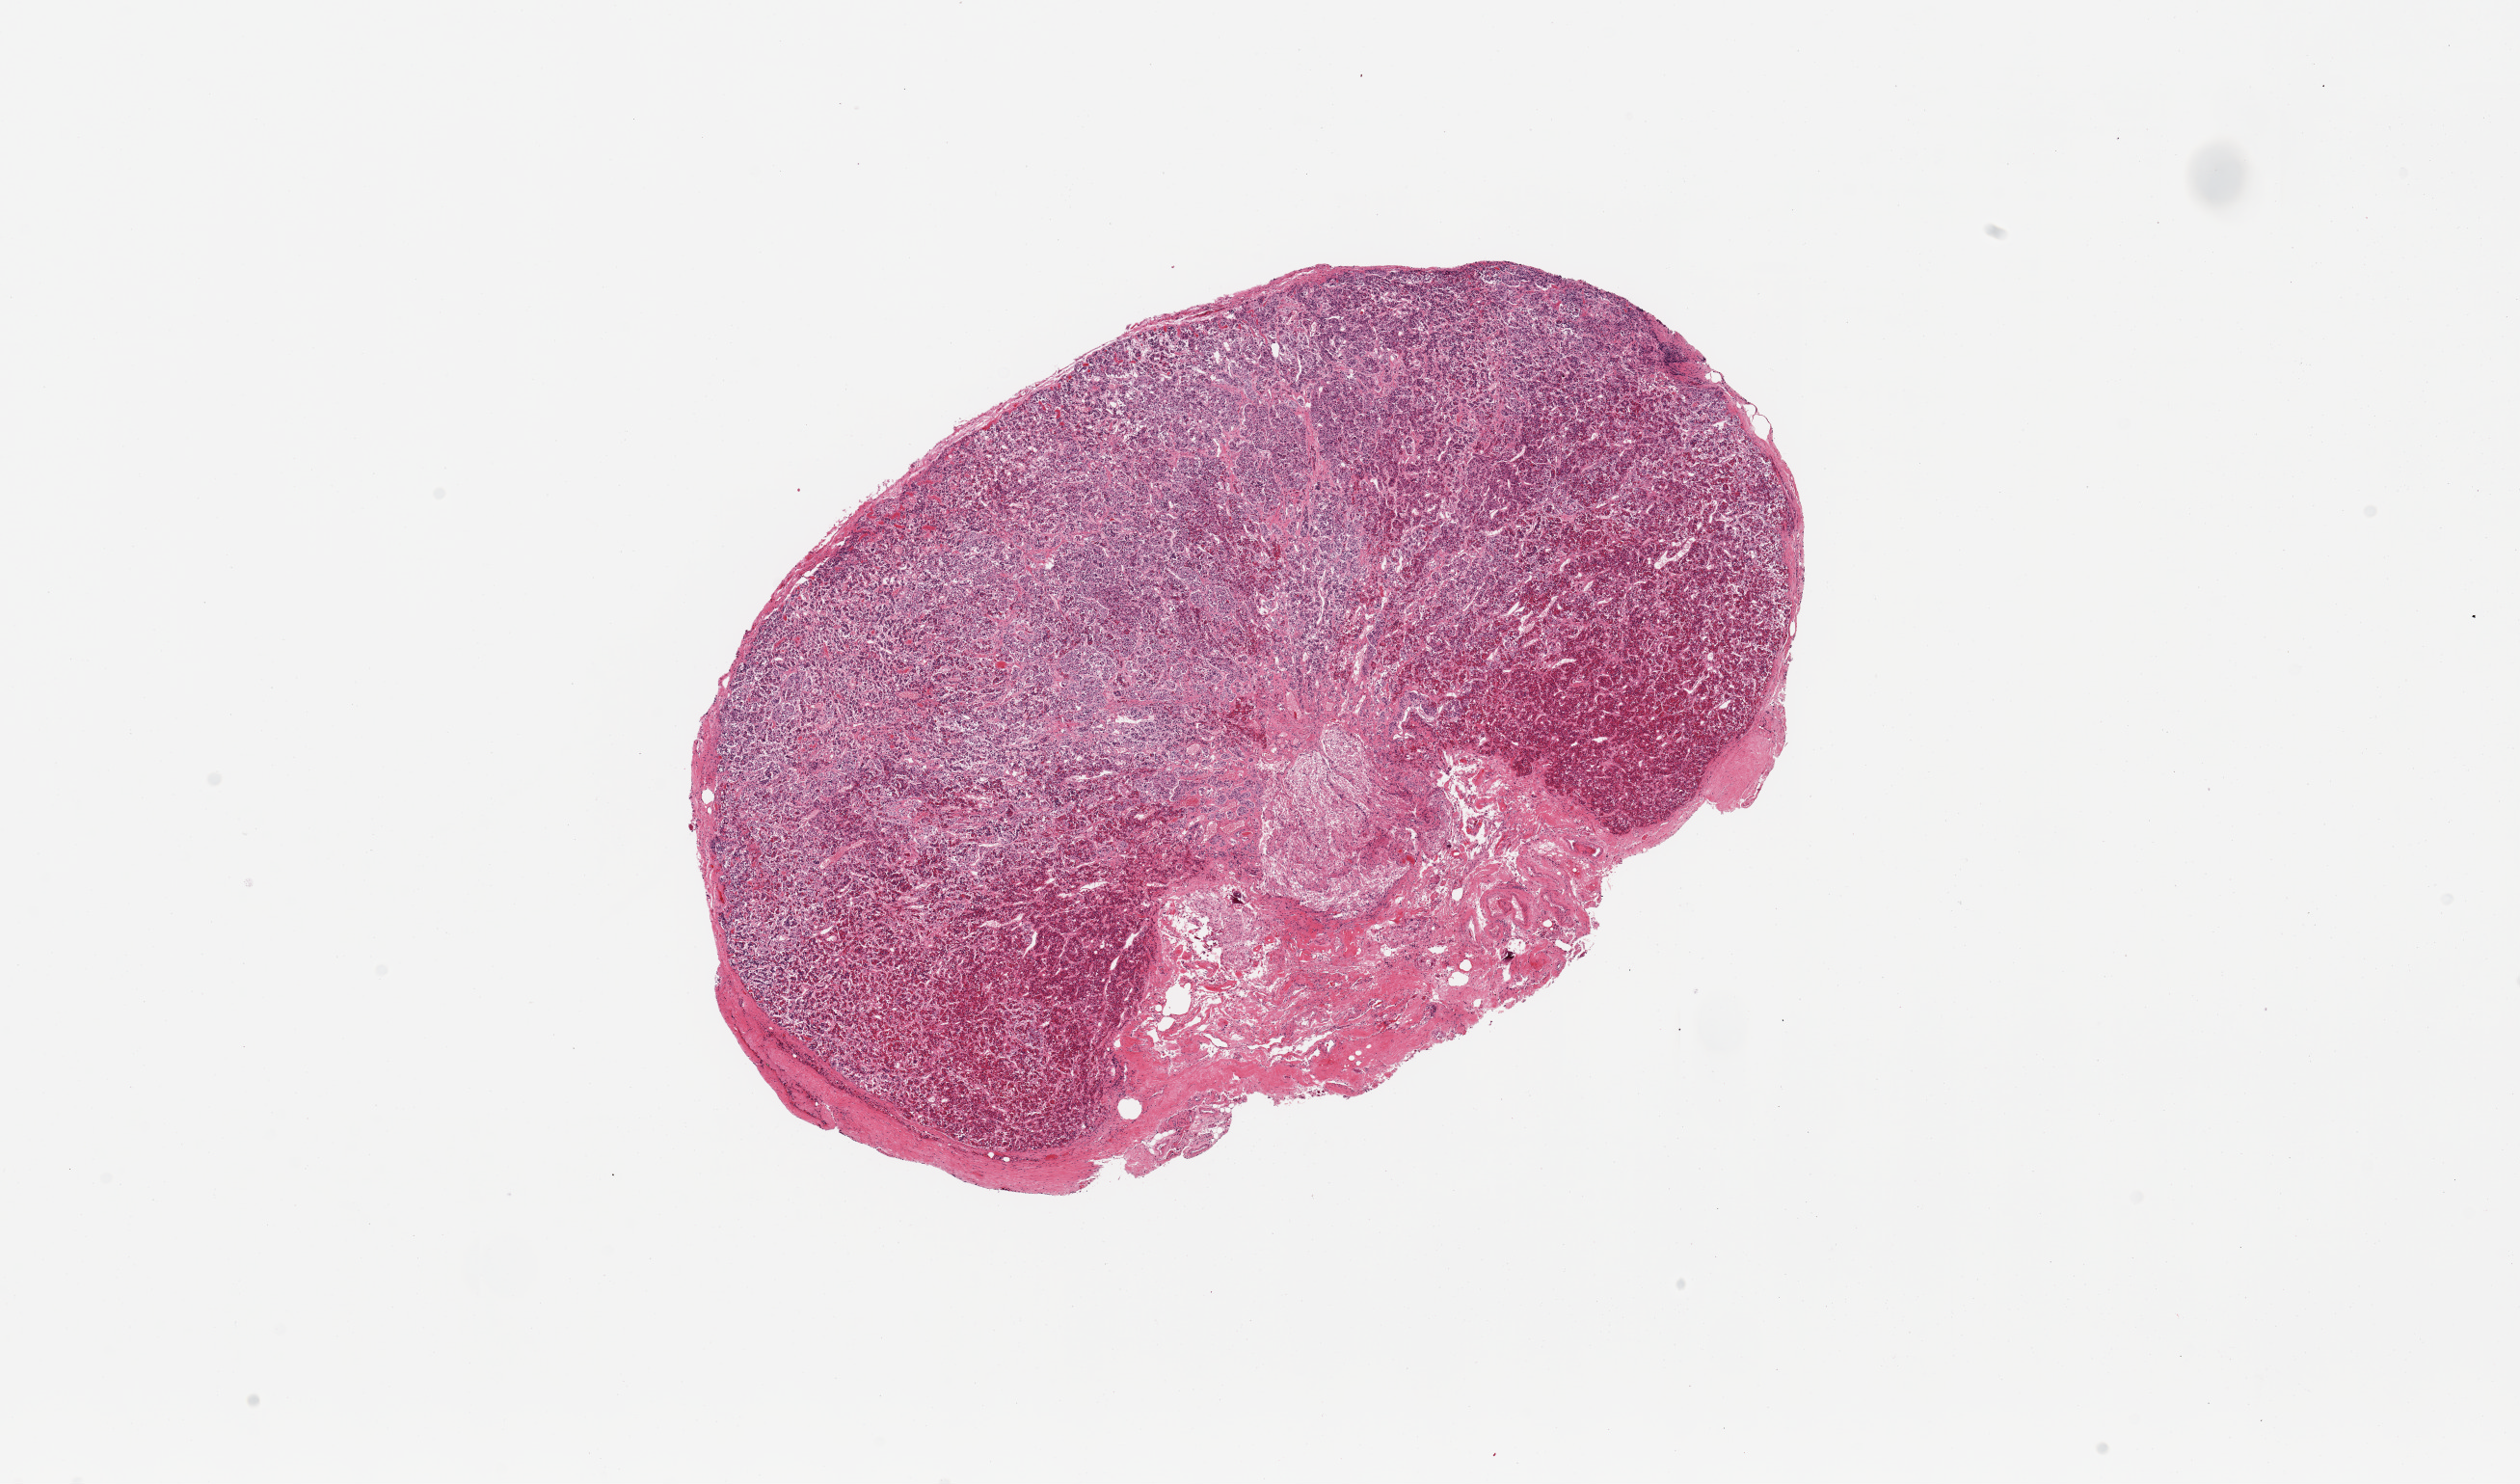
H&E whole-slide image, whole scanned area (about 20.7 x 12.2 mm) shown as a low-resolution overview, PAXgene-fixed, paraffin-embedded tissue, sampled site (target tissue): pituitary, donor tissue sample.
Pathologist's review note for this sample: 1 piece; anterior and posterior present.